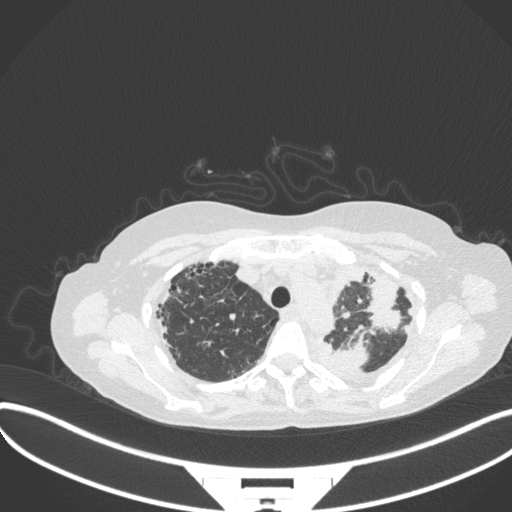
Chest CT, one axial slice. Position 272 of 373 along the scan axis. 120 kVp. Lung window (W 1500 / L -600 HU). 1 mm slice thickness. 512 × 512 image matrix, field of view 400 × 400 mm. Female patient, age 56 years. From the clinical record (not read from this slice): clinical TNM (as recorded): T1 N0 M0.
Structures marked on this image (bounding box drawn by a radiologist):
- lung tumour (recorded histology: adenocarcinoma): bounding box <332,332,370,373> (left, top, right, bottom; pixels)
- lung tumour (recorded histology: adenocarcinoma): <359,267,404,334>